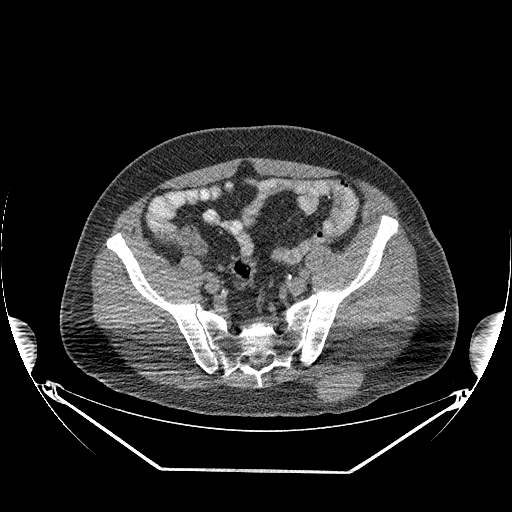
CT of an extremity soft-tissue mass (from a PET/CT study), one axial slice. Slice 83 of 267 in the series (ordered by position). Reconstruction kernel STANDARD. 140 kVp. Soft-tissue window (W 400 / L 40 HU). 512 × 512 image matrix. Male patient. Case-level facts recorded for this patient, not image findings: histological type: pleiomorphic leiomyosarcoma; grade: high; site of the primary tumour: left buttock.
Outlined on this slice (expert contour drawn on MRI and transferred to this co-registered scan by the dataset authors):
- gross tumour volume including surrounding oedema: box from (x=317, y=373) to (x=364, y=403) px
- gross tumour volume (mass): (x=322, y=375)–(x=362, y=401)